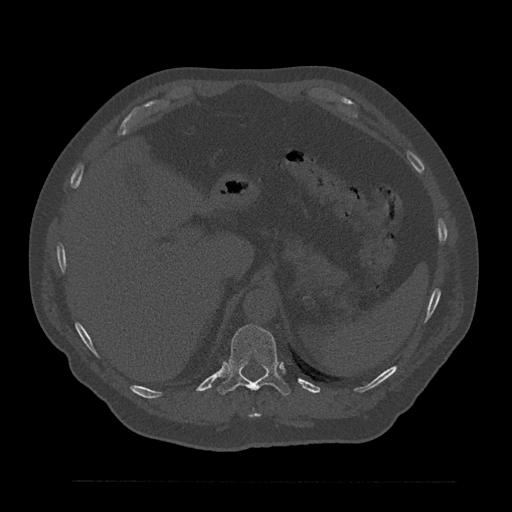
CT including the spine, one axial slice; position 300 of 797 along the scan axis; reconstruction kernel Br40s/3; bone window (W 1800 / L 400 HU); 0.5 mm slice thickness; 512 × 512 image matrix, field of view 430 × 430 mm. Male patient, age 61 years. Case-level facts recorded for this patient, not image findings: primary cancer: prostate.
Annotated regions visible in this slice (semi-automatic segmentation, software-assisted and operator-edited):
- T10 vertebra: bounding box [x1, y1, x2, y2] px = [249, 413, 260, 418]
- T11 vertebra: [218, 325, 291, 396]